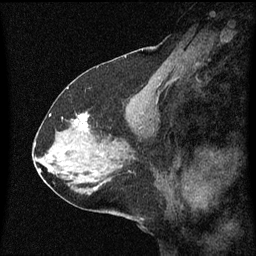
Breast MRI (dynamic contrast-enhanced), one sagittal slice. Position 30 of 60 along the scan axis. Dynamic contrast-enhanced series, image 2 of 3 at this slice position (ordered by acquisition). 1.5 T. TE 4.2 ms, TR 8.4 ms. 256 × 256 image matrix, field of view 200 × 200 mm. Female patient, age 59 years.
Annotated regions visible in this slice (semi-automatic segmentation, software-assisted and operator-edited):
- analysis volume of interest (the breast-tissue region the enhancement analysis was run in; not a lesion): bounding box <70,112,94,137> (left, top, right, bottom; pixels)
- tumour enhancement mask (voxels above the 70 % enhancement threshold inside the analysis volume of interest): <75,112,89,129>